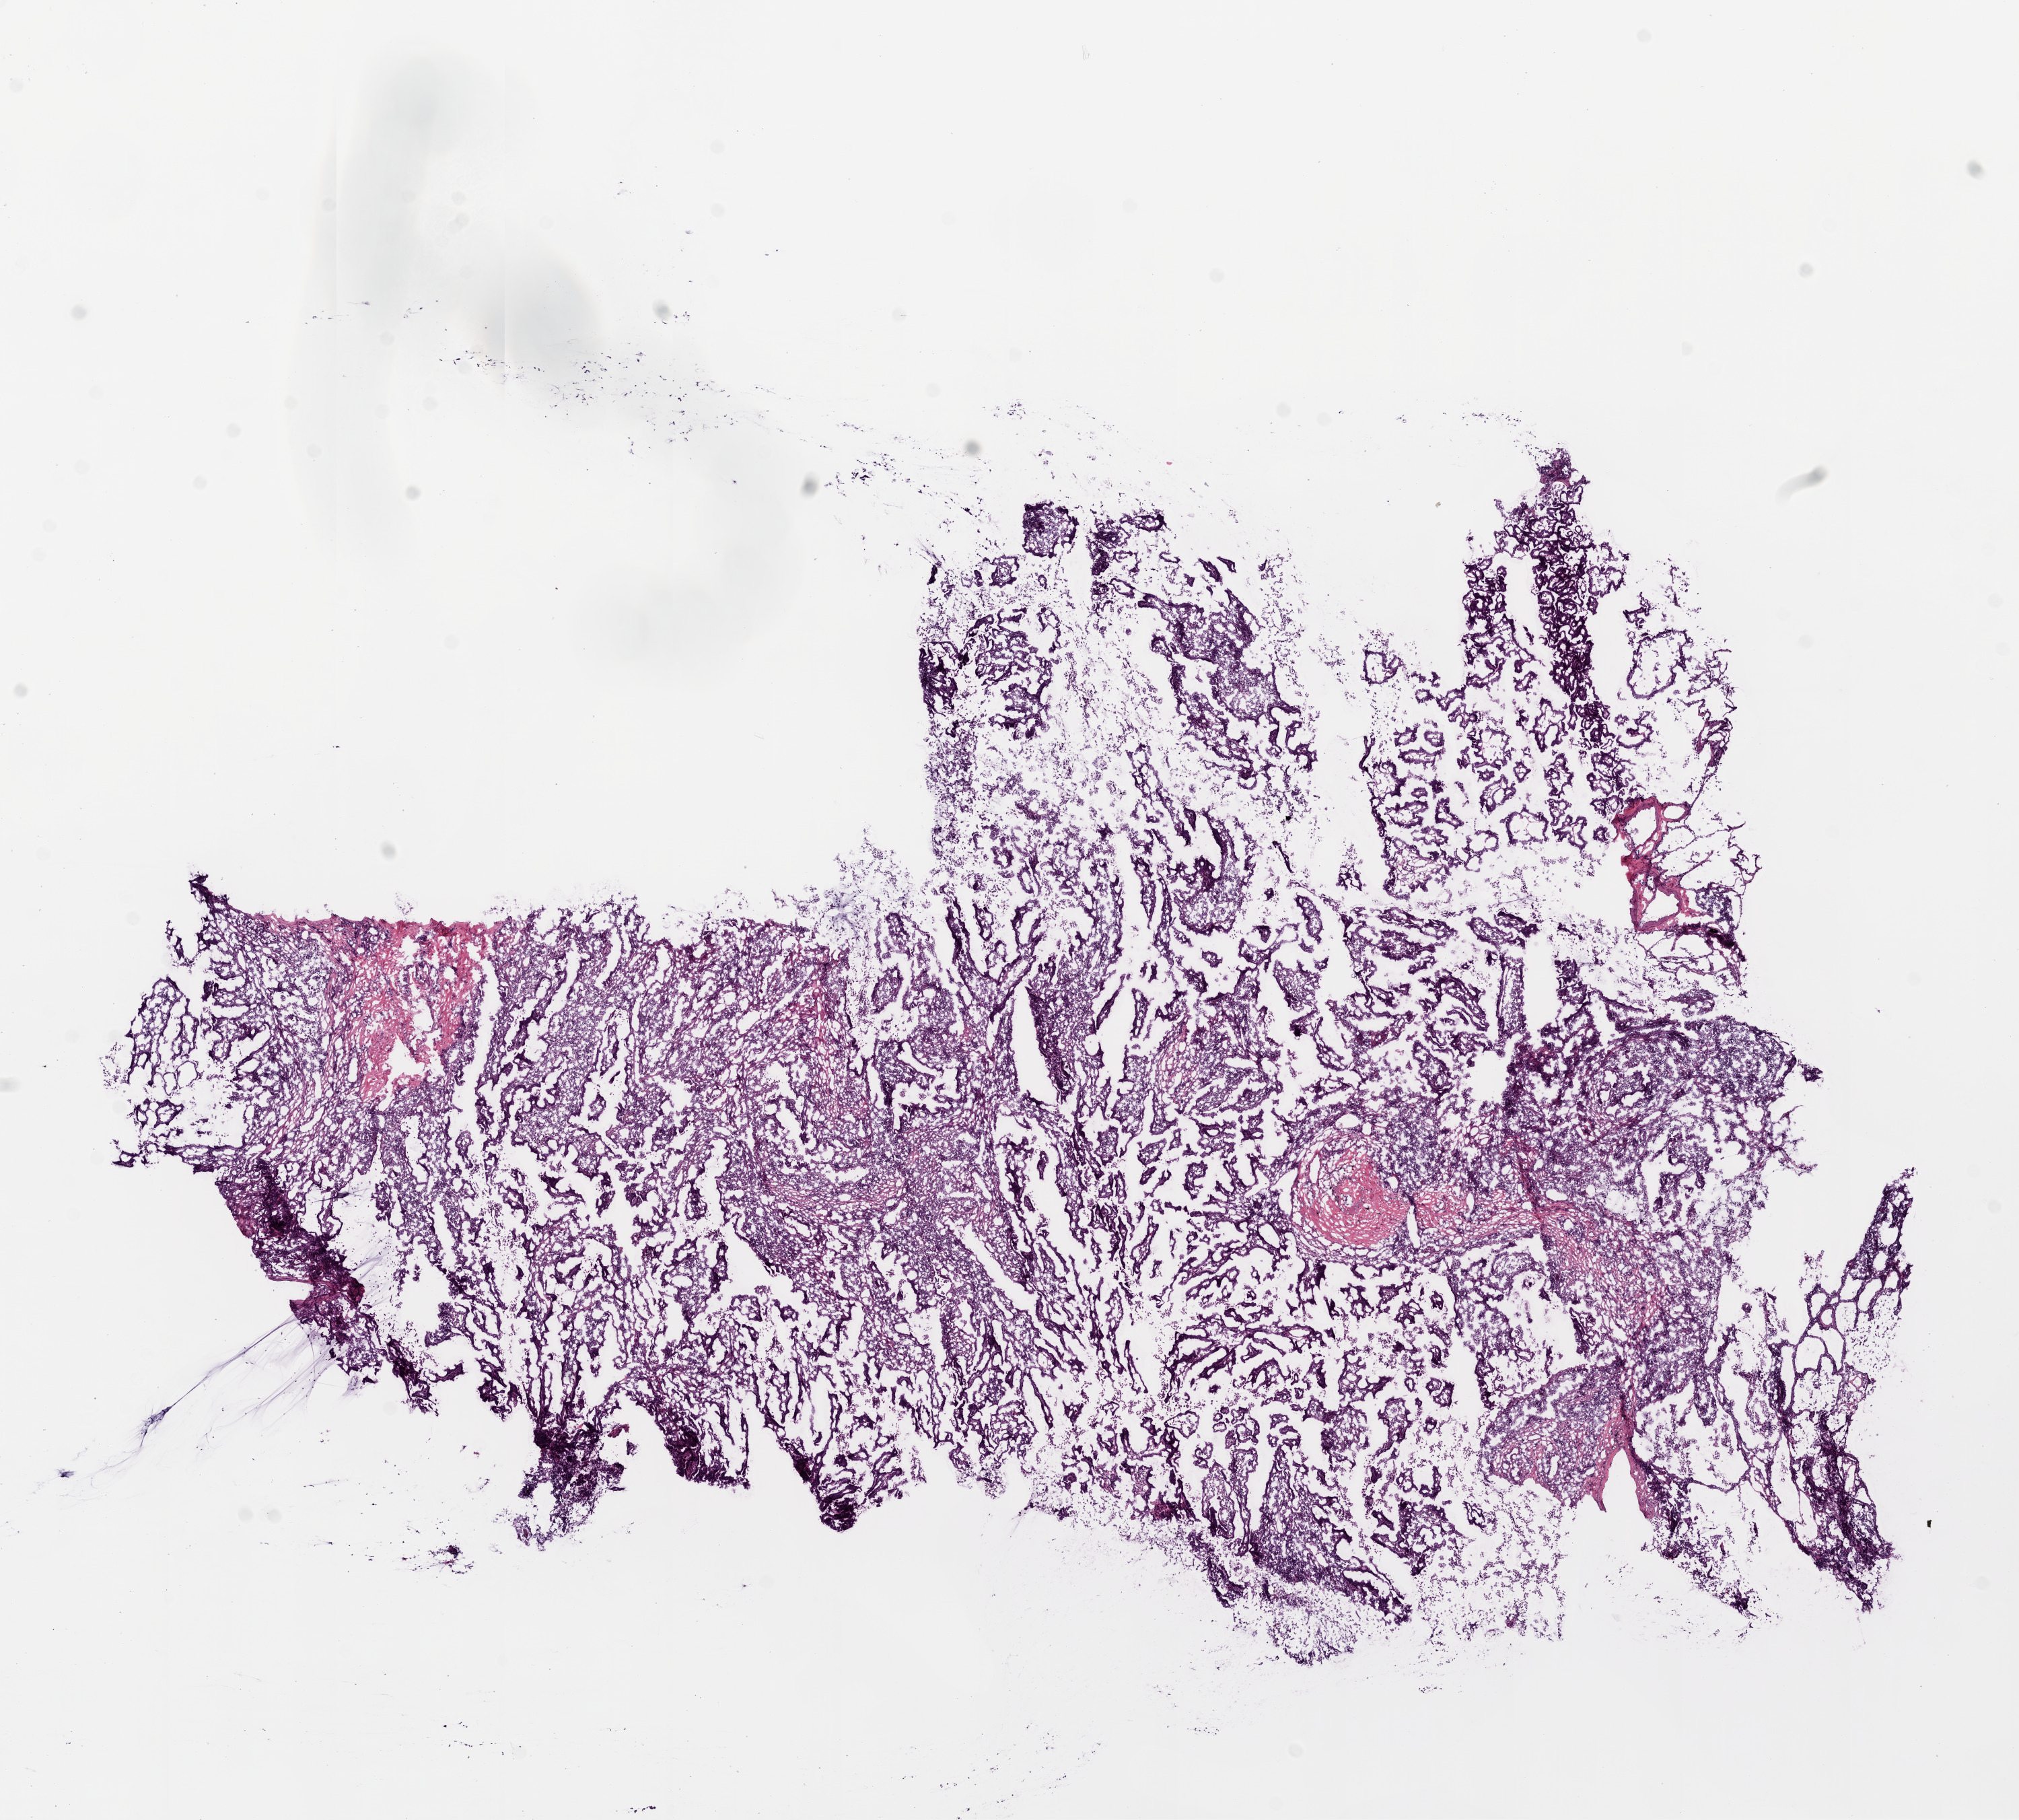
H&E-stained whole-slide image — whole scanned area (about 12.0 x 10.8 mm) shown as a low-resolution overview; frozen section; sample: primary tumour, lung. Female, age 79 years at initial diagnosis. Composition of this section per pathologist review: tumour cells 85%, tumour nuclei 60%, normal cells 10%, stromal cells 5%, necrosis 0%.
Laterality: left. AJCC pathologic stage: IA. Histologic diagnosis: Papillary adenocarcinoma, NOS.